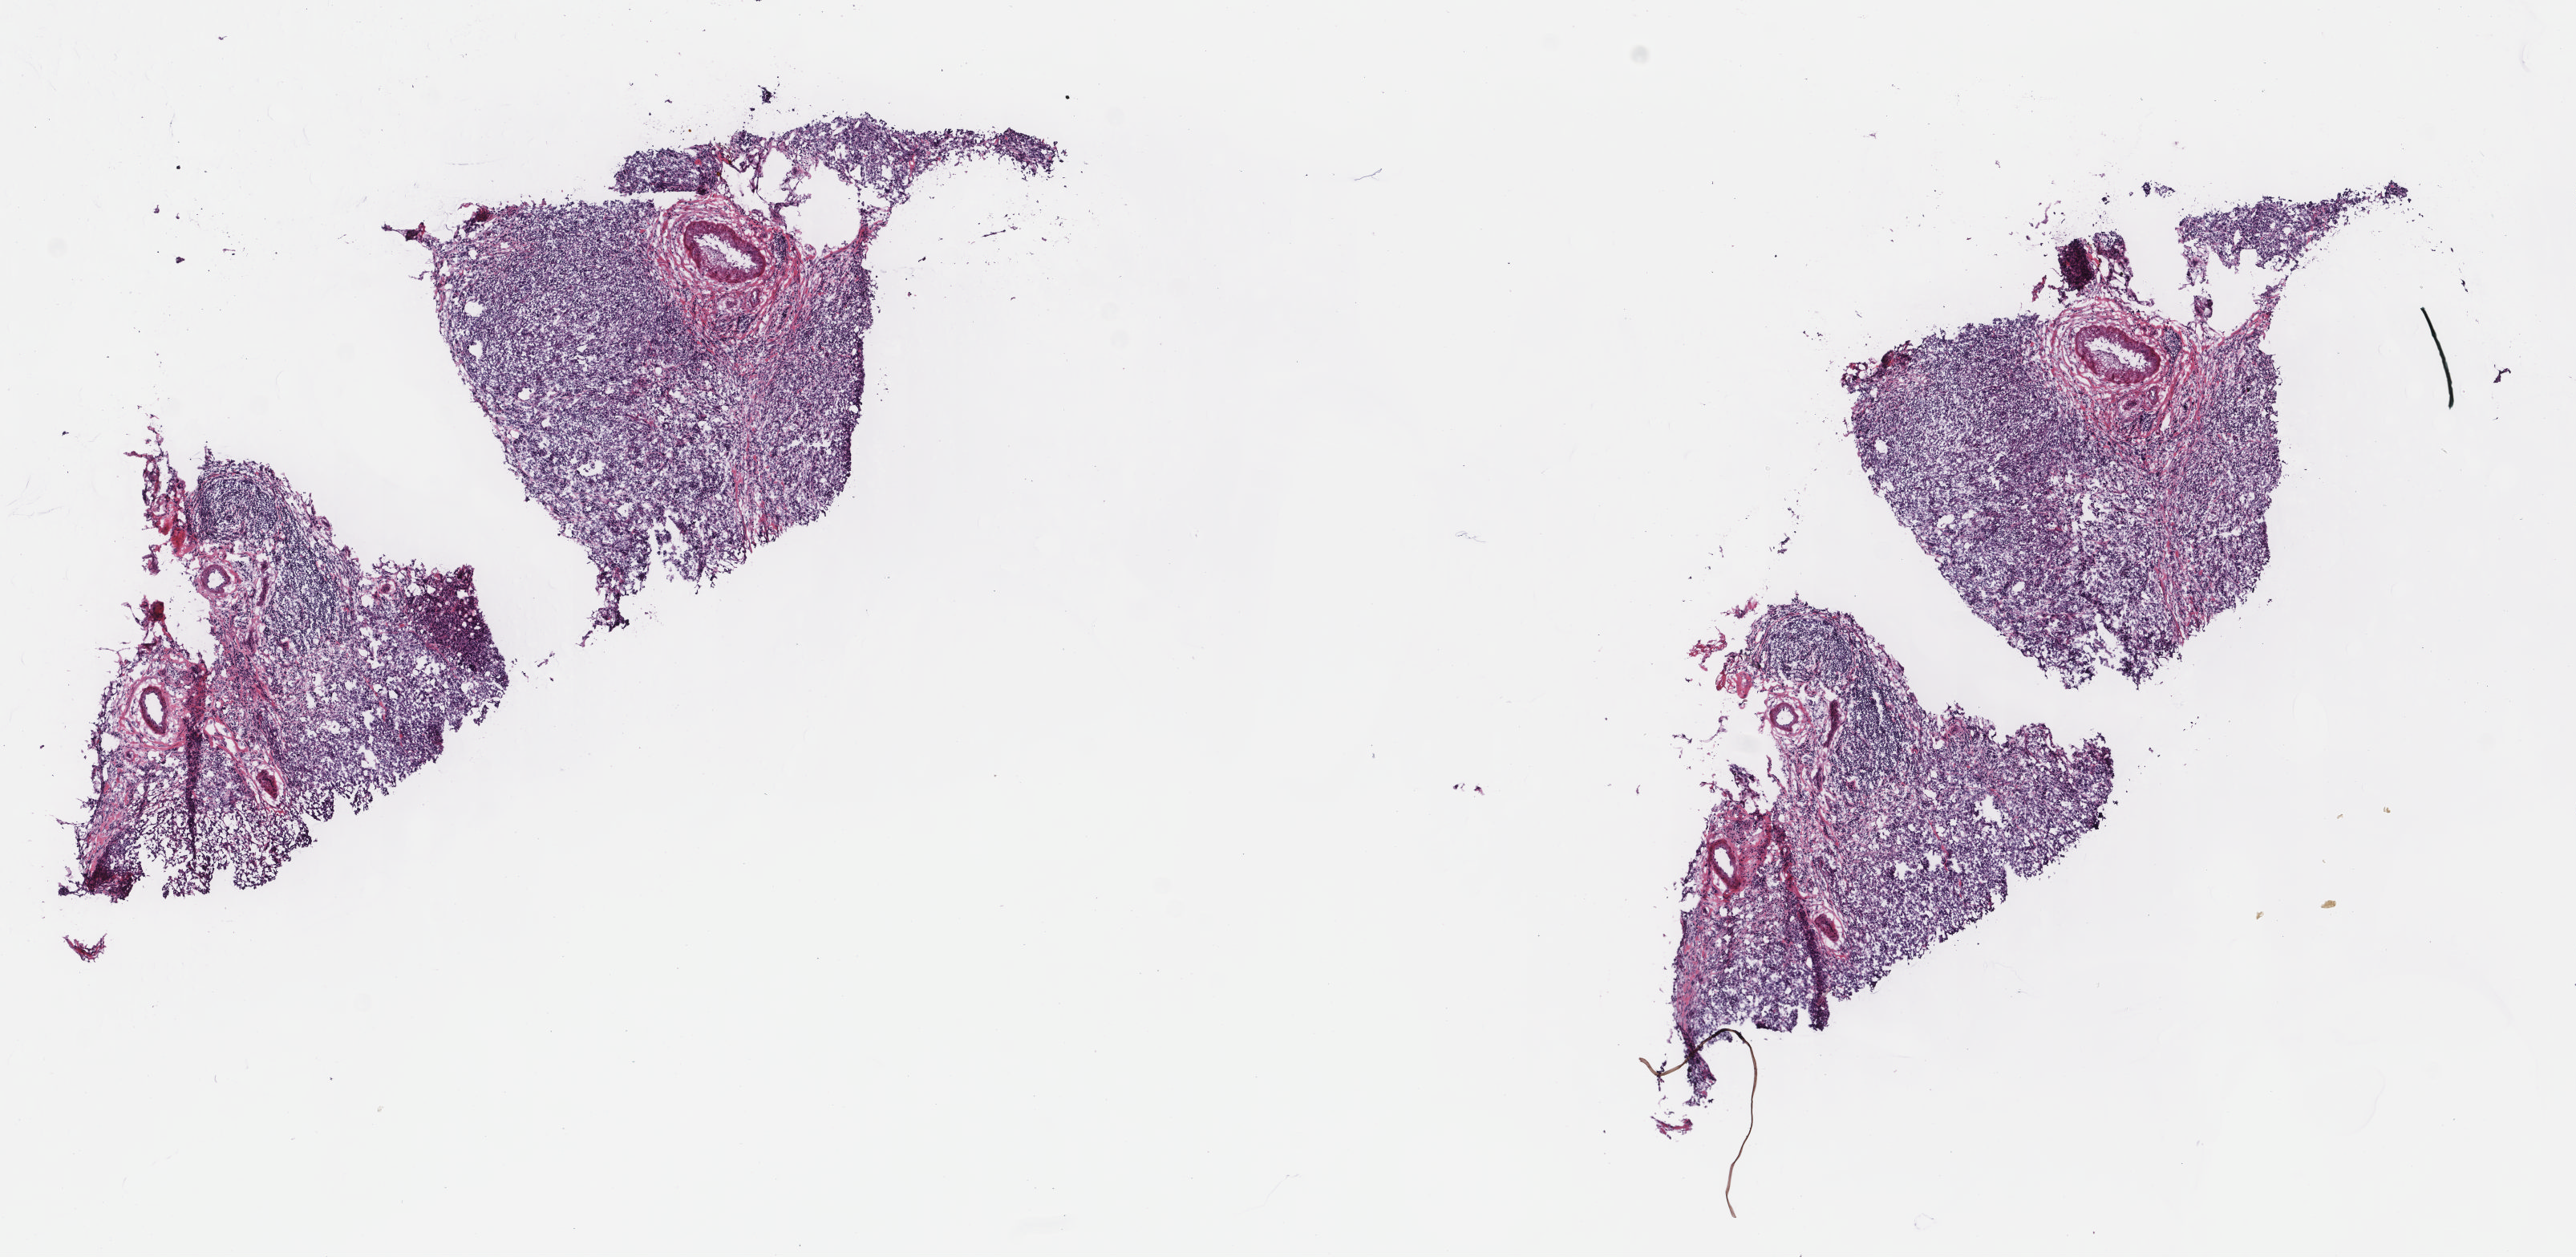
Whole-slide histology image, Hematoxylin and eosin (H&E) stained, low-resolution overview of the scanned area, about 12.7 x 6.2 mm; frozen section from the top of the tissue portion; breast, primary tumour sample. Patient: female, age at initial diagnosis 66 years. Slide review estimates, as recorded: tumour cells 65%, tumour nuclei 75%, normal cells 0%, stromal cells 35%, necrosis 0%. Inflammatory infiltration, as recorded: lymphocyte infiltration 10%, monocyte infiltration 0%, neutrophil infiltration 0%.
Diagnosis: Infiltrating duct carcinoma, NOS. AJCC pathologic stage: IIA (7th edition). TNM: T2 N0 (i-) M0.